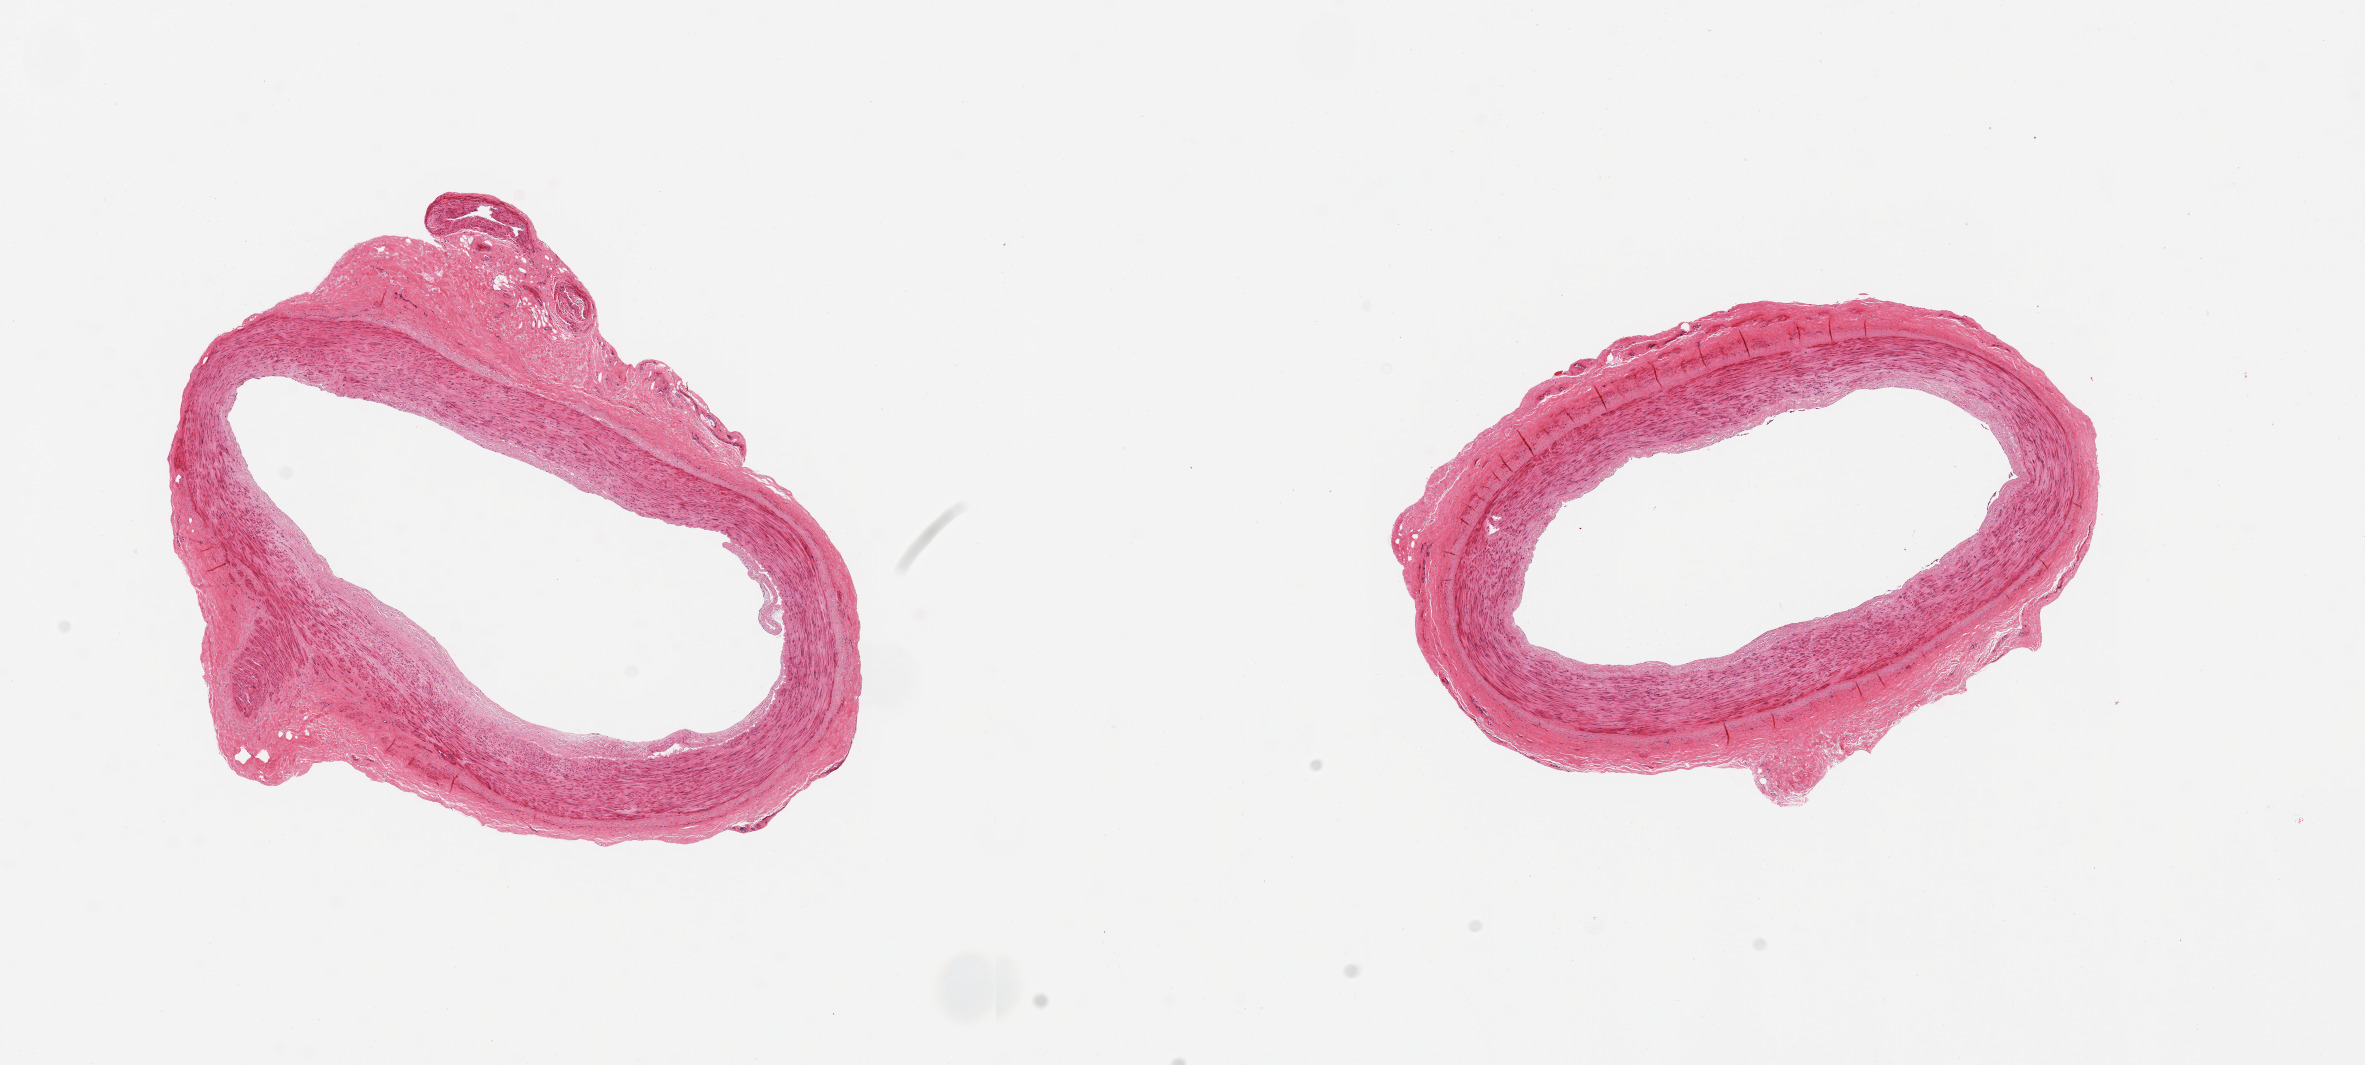
Digitized hematoxylin and eosin (H&E)-stained section, brightfield — shown as a low-resolution overview of the whole scanned area (about 18.7 x 8.4 mm), PAXgene-fixed paraffin-embedded (PFPE) section, sampled site (target tissue): tibial artery, donor tissue sample. Female donor.
Review note (as recorded): 2 pieces; attached adventitia up to 1mm; focal intimal thickening.